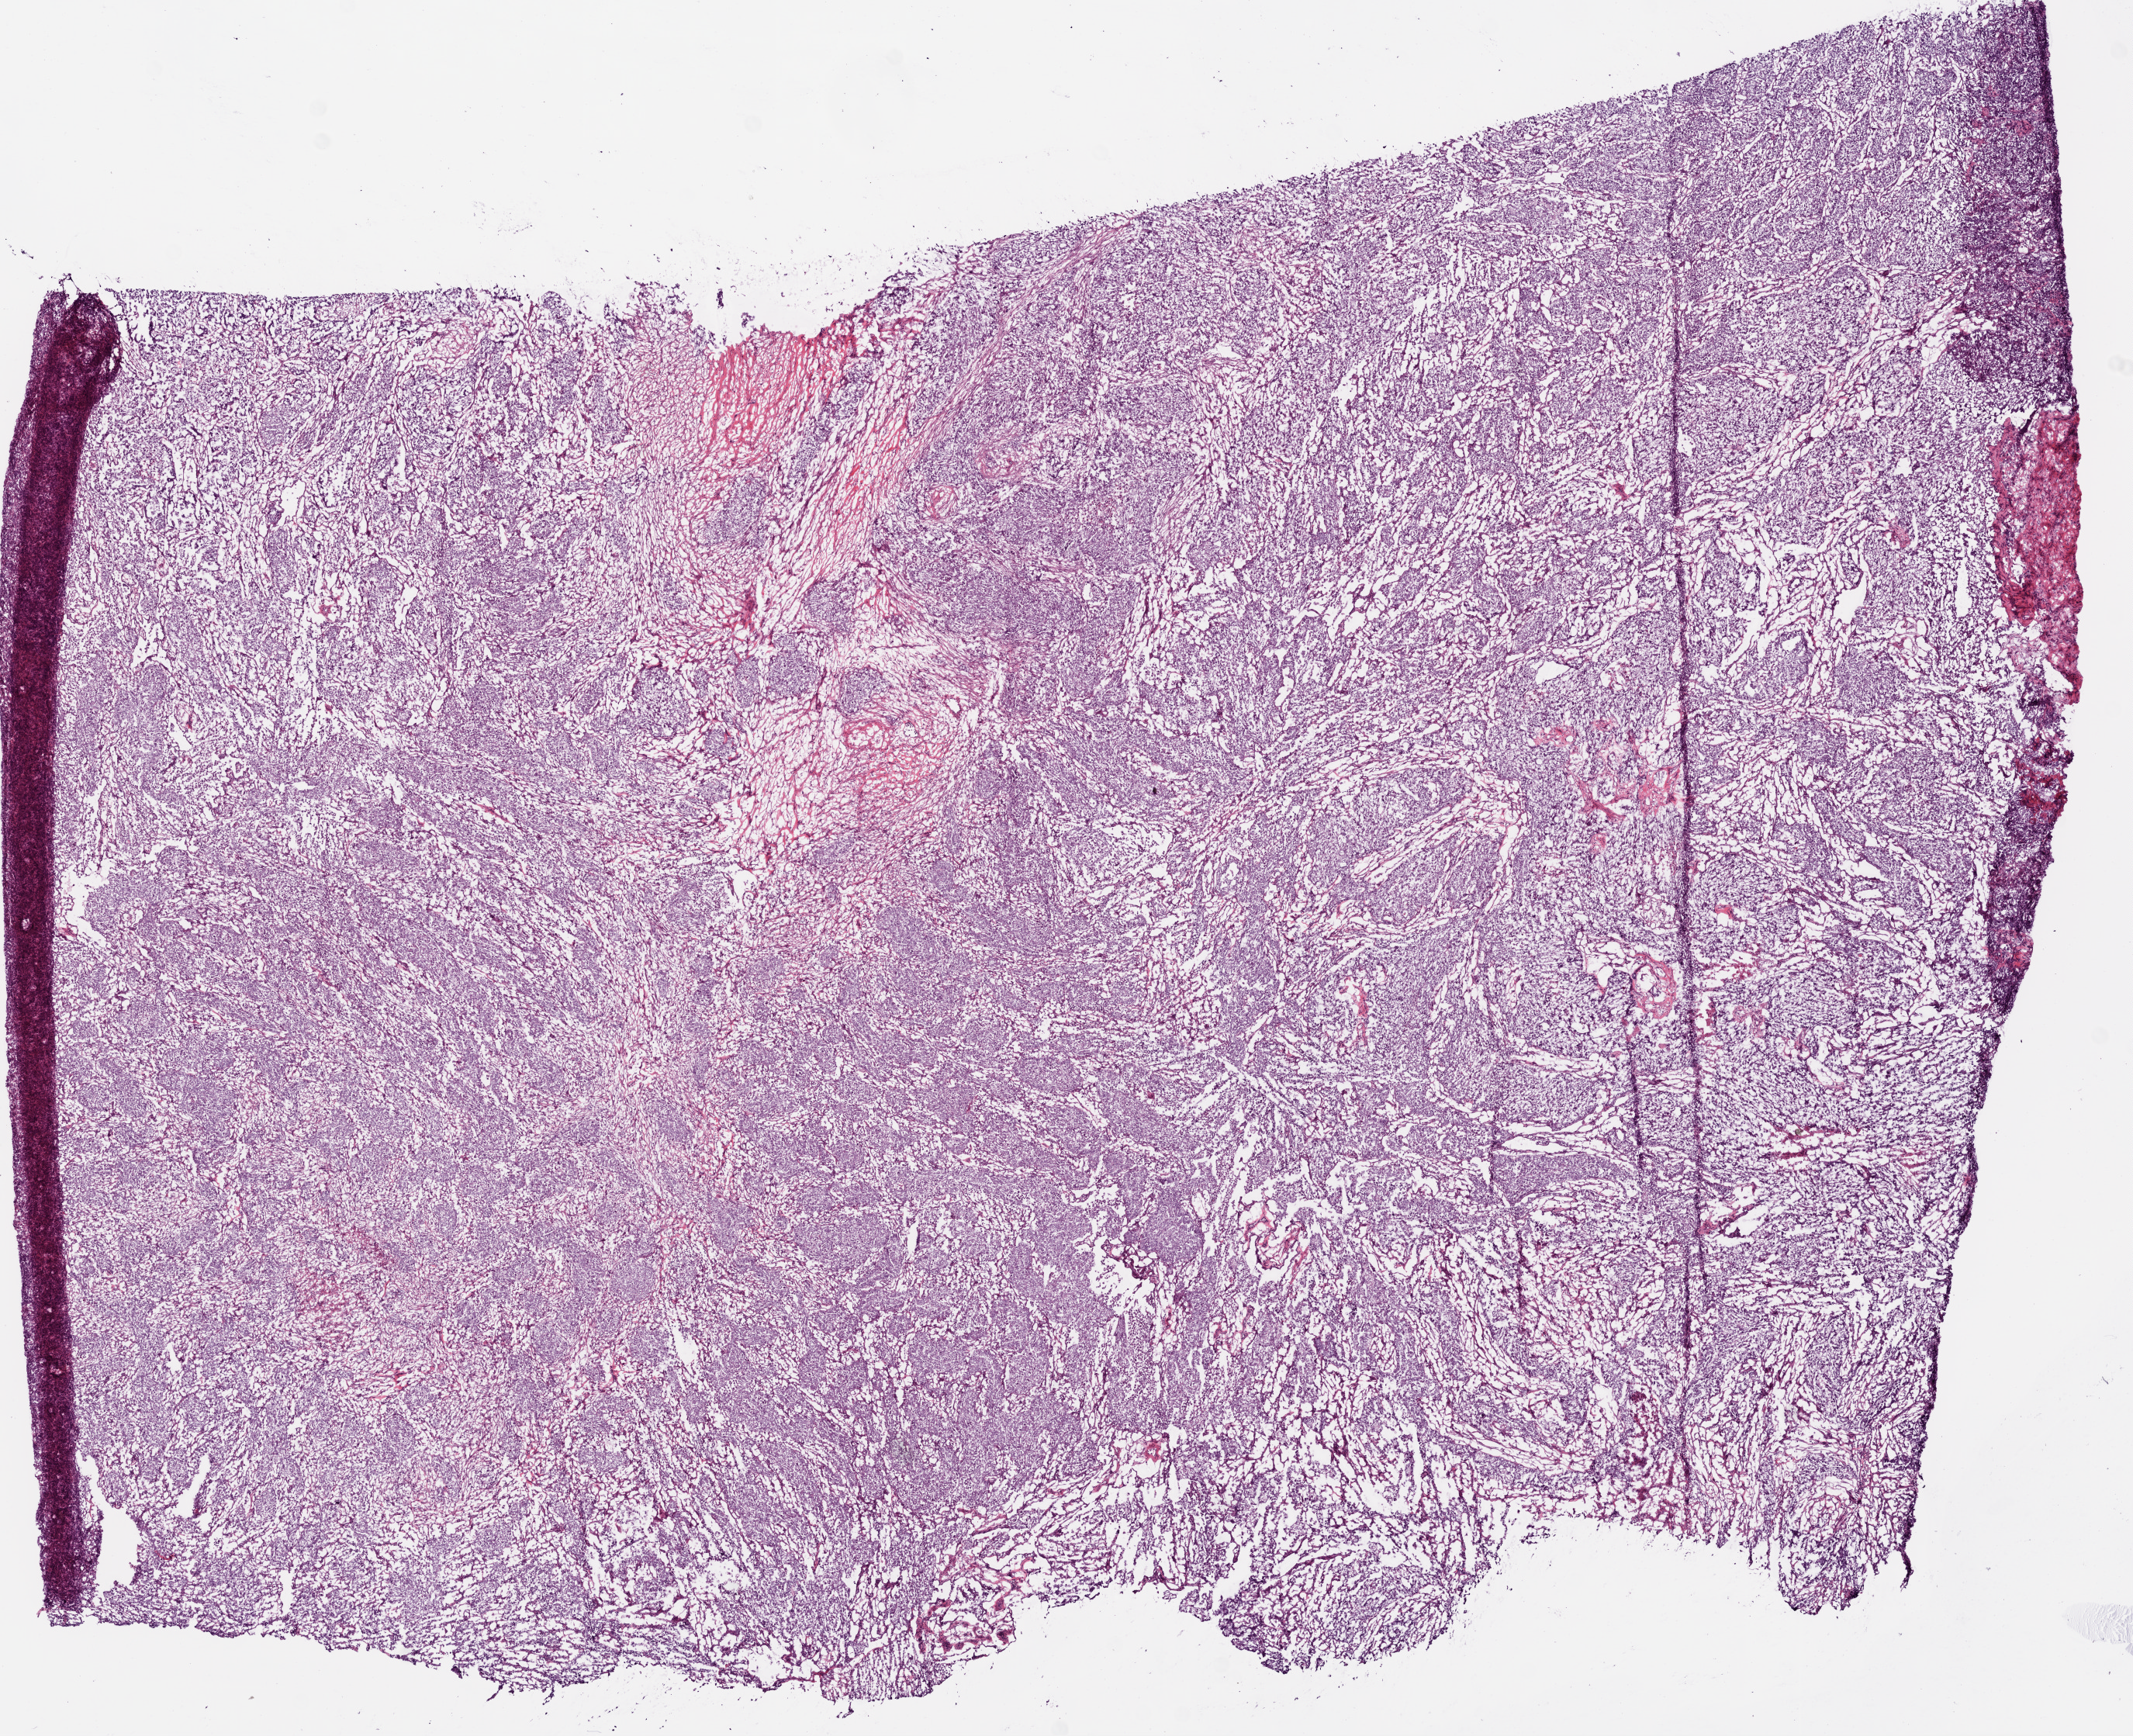
Whole-slide histology image, H&E-stained — whole scanned area (about 11.0 x 9.0 mm, slide scanned at 20x) shown as a low-resolution overview; frozen section from the bottom of the tissue portion; sample: primary tumour, ovary. Patient: female, age at initial diagnosis 67 years. Histologic grade: G3 (poorly differentiated). Composition of this section per pathologist review: tumour cells 89%, tumour nuclei 90%, normal cells 0%, stromal cells 10%, necrosis 1%.
FIGO stage: IIIC. Pathologic diagnosis: Serous cystadenocarcinoma, NOS.